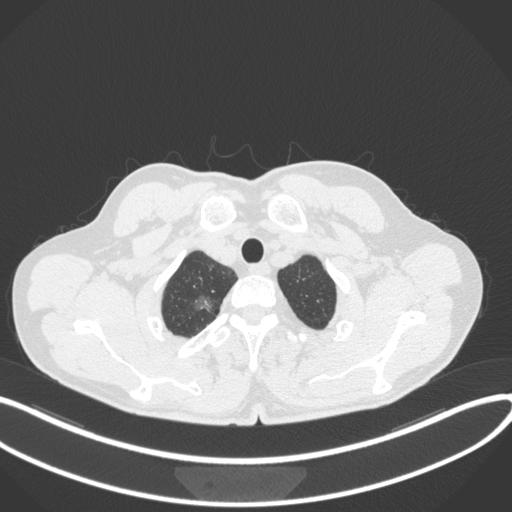
Chest CT, one axial slice. Position 351 of 407 along the scan axis. Reconstruction kernel B31f. 120 kVp. Lung window (W 1500 / L -600 HU). 512 × 512 image matrix, field of view 400 × 400 mm. Patient: male, 58 years. From the clinical record (not read from this slice): clinical TNM (as recorded): T1c N0 M0.
Annotated regions visible in this slice (rectangle marked by the reading radiologist):
- lung tumour (recorded histology: adenocarcinoma): bounding box [x1, y1, x2, y2] px = [187, 289, 219, 314]